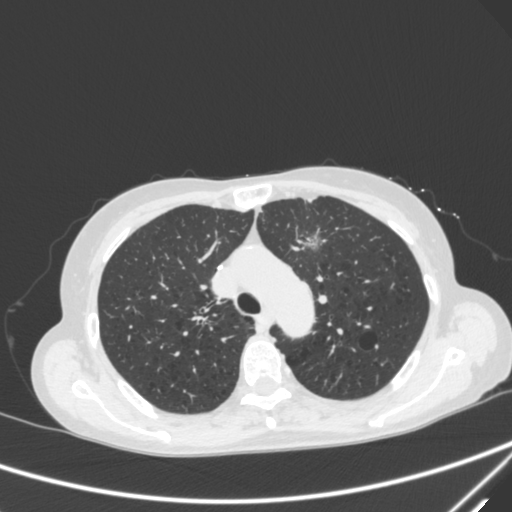
Chest CT, one axial slice. Slice 219 of 300 in the series (ordered by position). 120 kVp. Lung window (W 1500 / L -600 HU). 1 mm slice thickness. 512 × 512 image matrix, field of view 350 × 350 mm. Patient: female, 71 years. Case-level facts recorded for this patient, not image findings: clinical TNM (as recorded): T1c N0 M0; histopathological grade: G2-3.
Outlined on this slice (bounding box drawn by a radiologist):
- lung tumour (recorded histology: adenocarcinoma): bounding box [x1, y1, x2, y2] px = [301, 228, 328, 256]